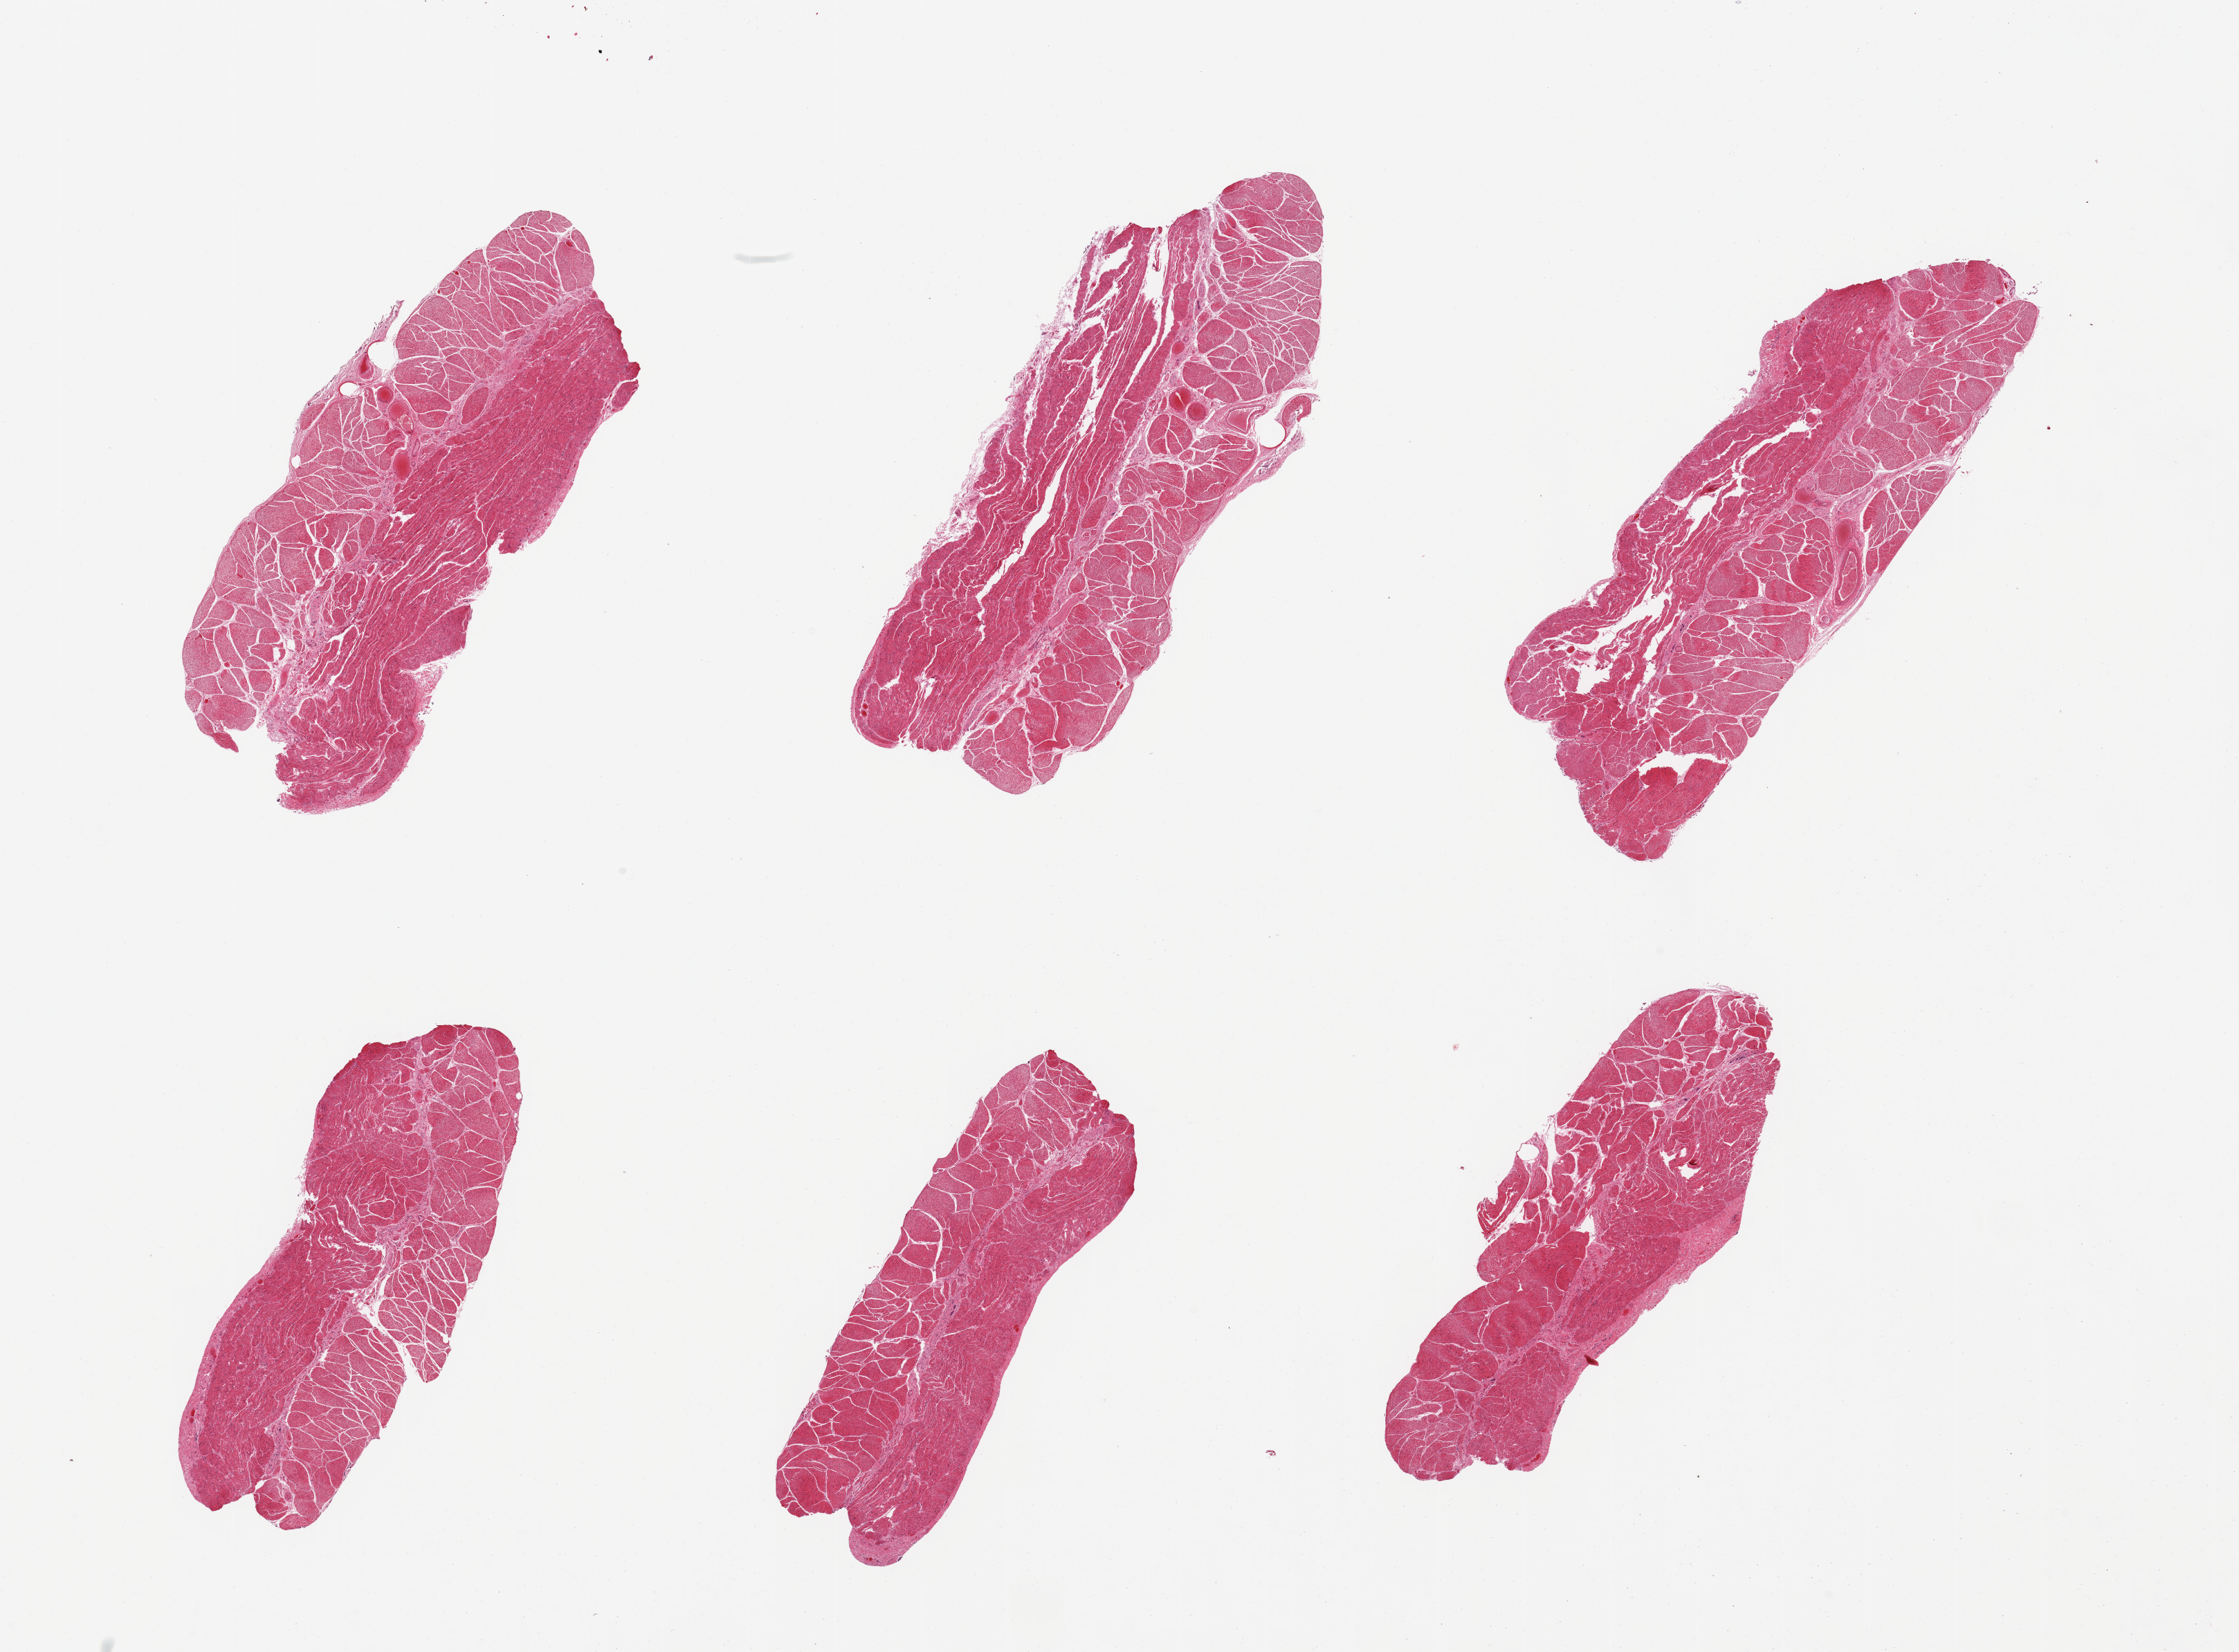
Whole-slide image, H&E stain — whole scanned area (about 25.6 x 18.9 mm, from a 20x scan) shown as a low-resolution overview; PAXgene-fixed, paraffin-embedded tissue; section of esophageal muscle (target tissue); tissue donor sample. Donor: male.
Reviewer comment on this tissue sample: 6 pieces, confirmed target muscularis.